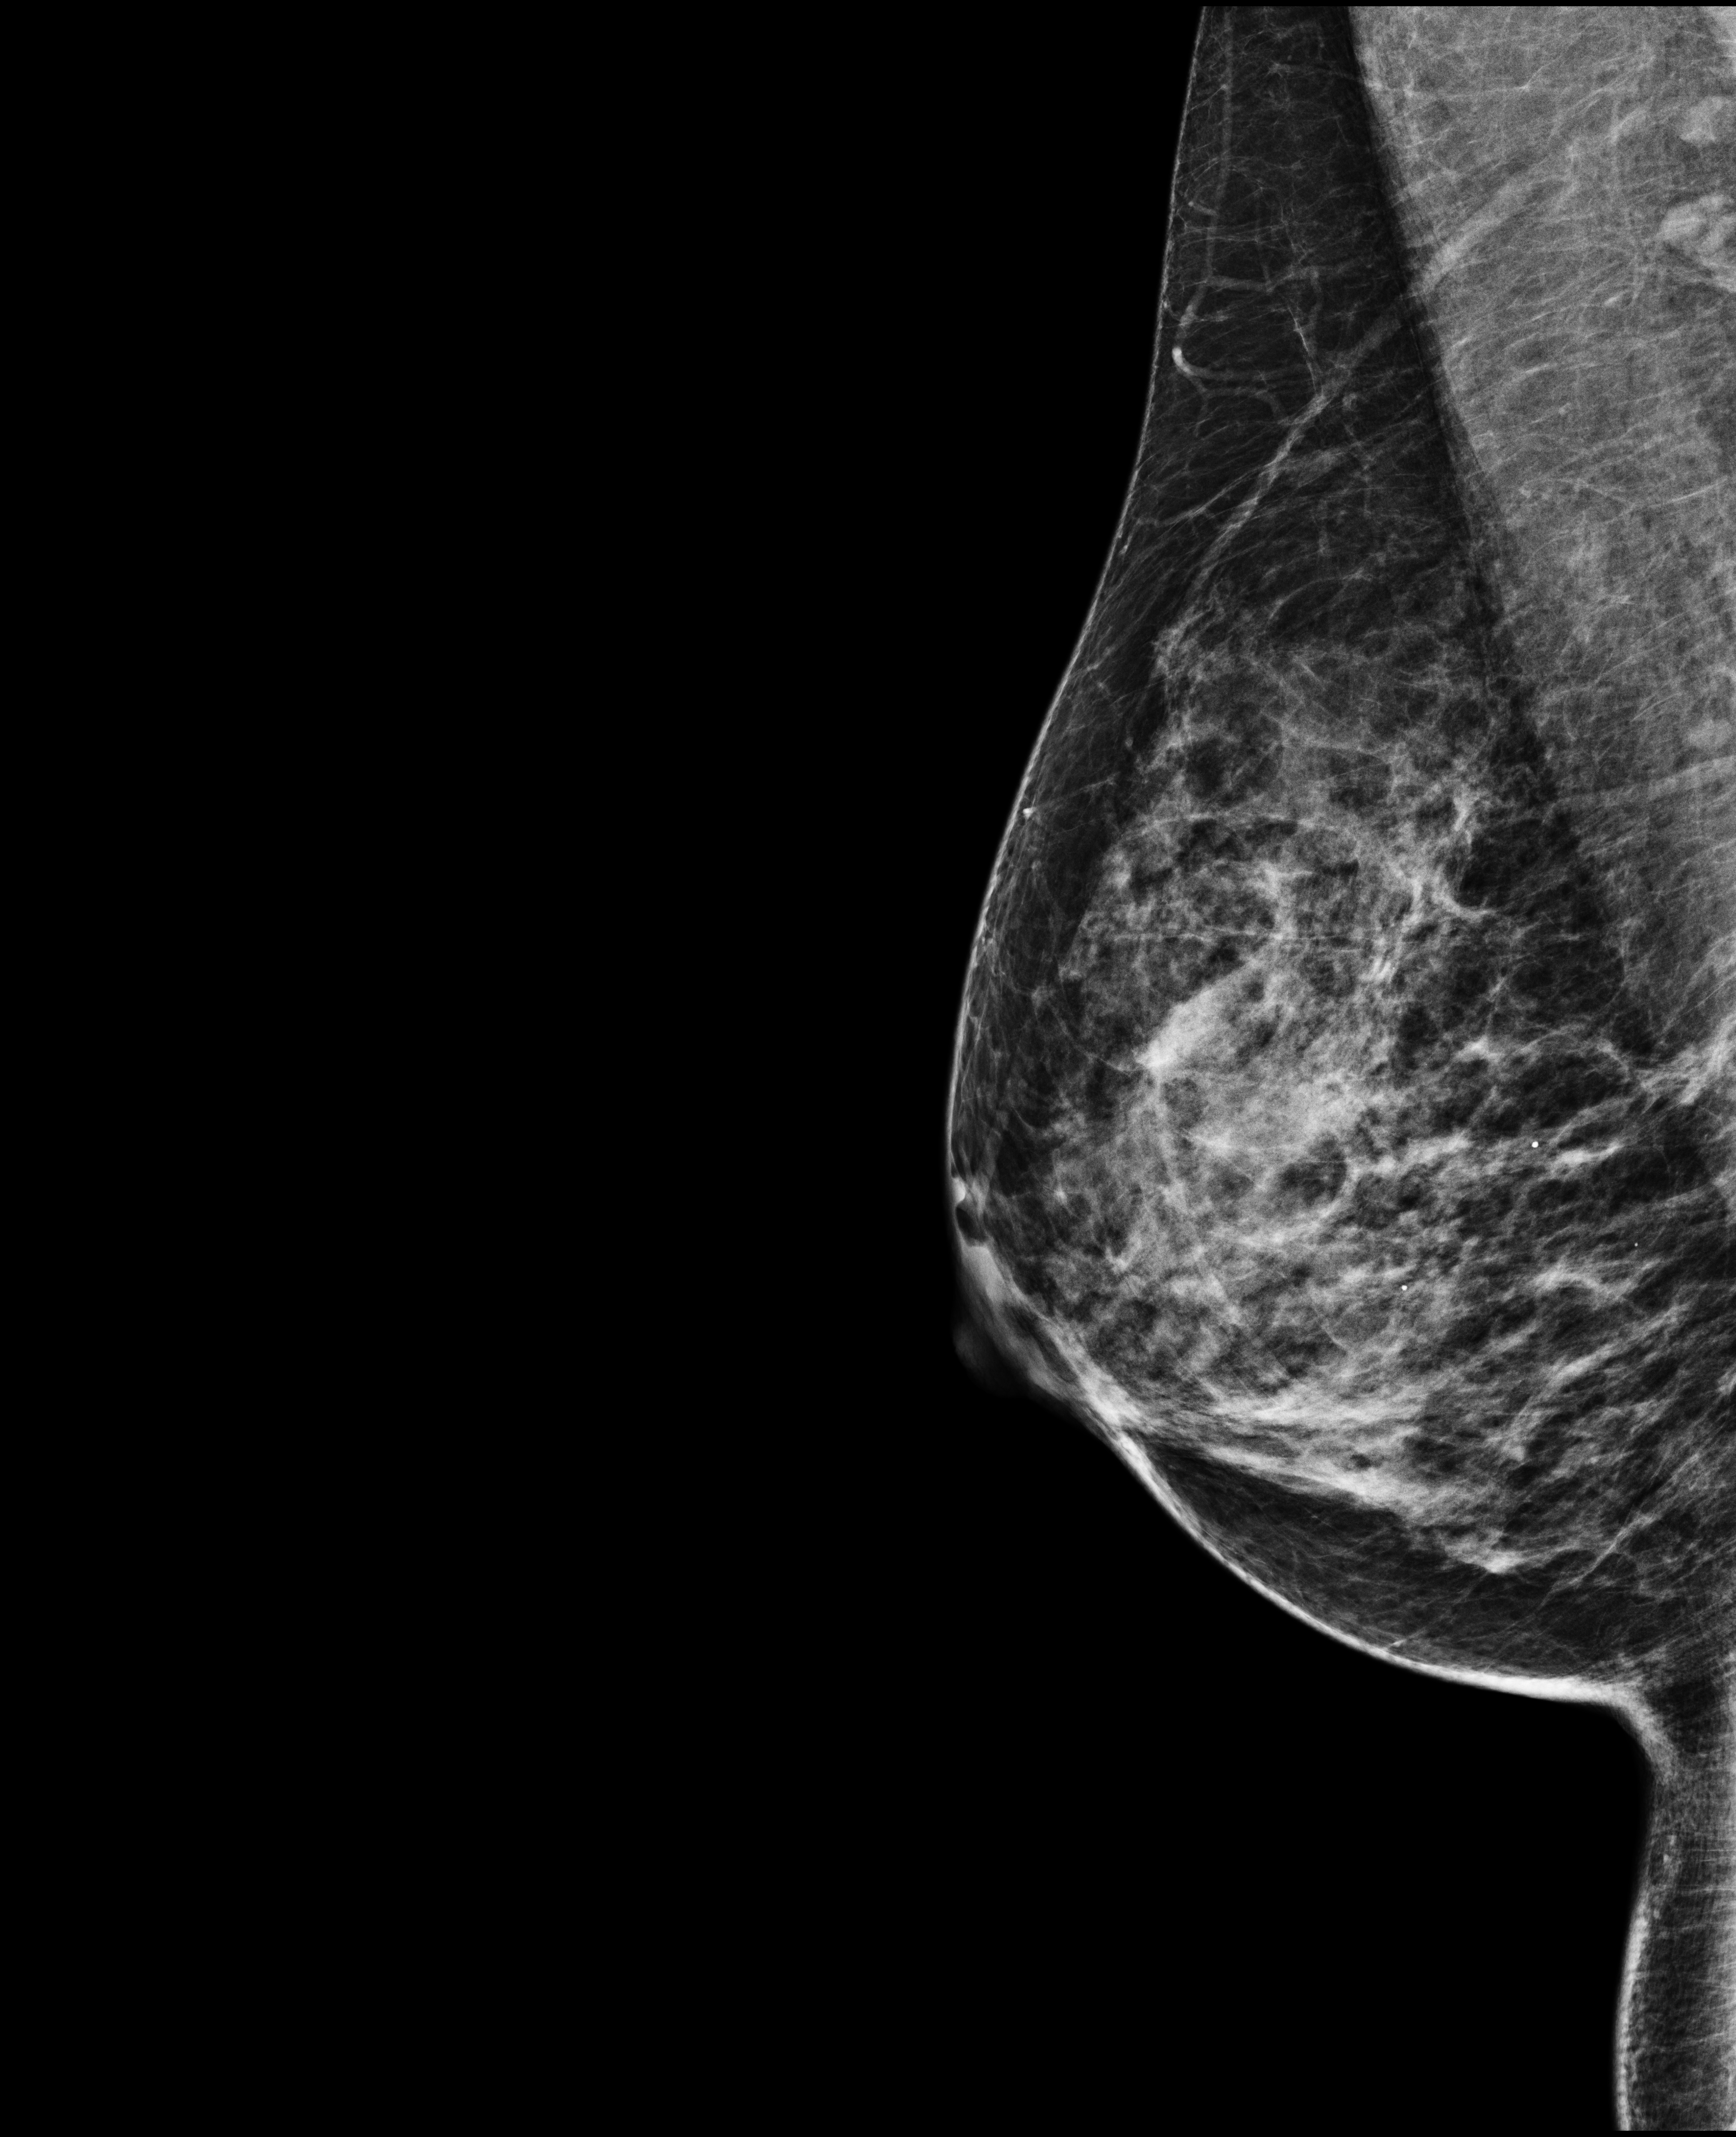
Full-field digital mammogram (FFDM); right breast; MLO view; screening examination; compressed breast thickness 50 mm. Patient: female, 46 years.
Breast density at the screening exam (both breasts): heterogeneously dense (BI-RADS density category c). Final BI-RADS category for the screening round (tomosynthesis exam, both breasts): category 1. Recall: no recall after this screen.